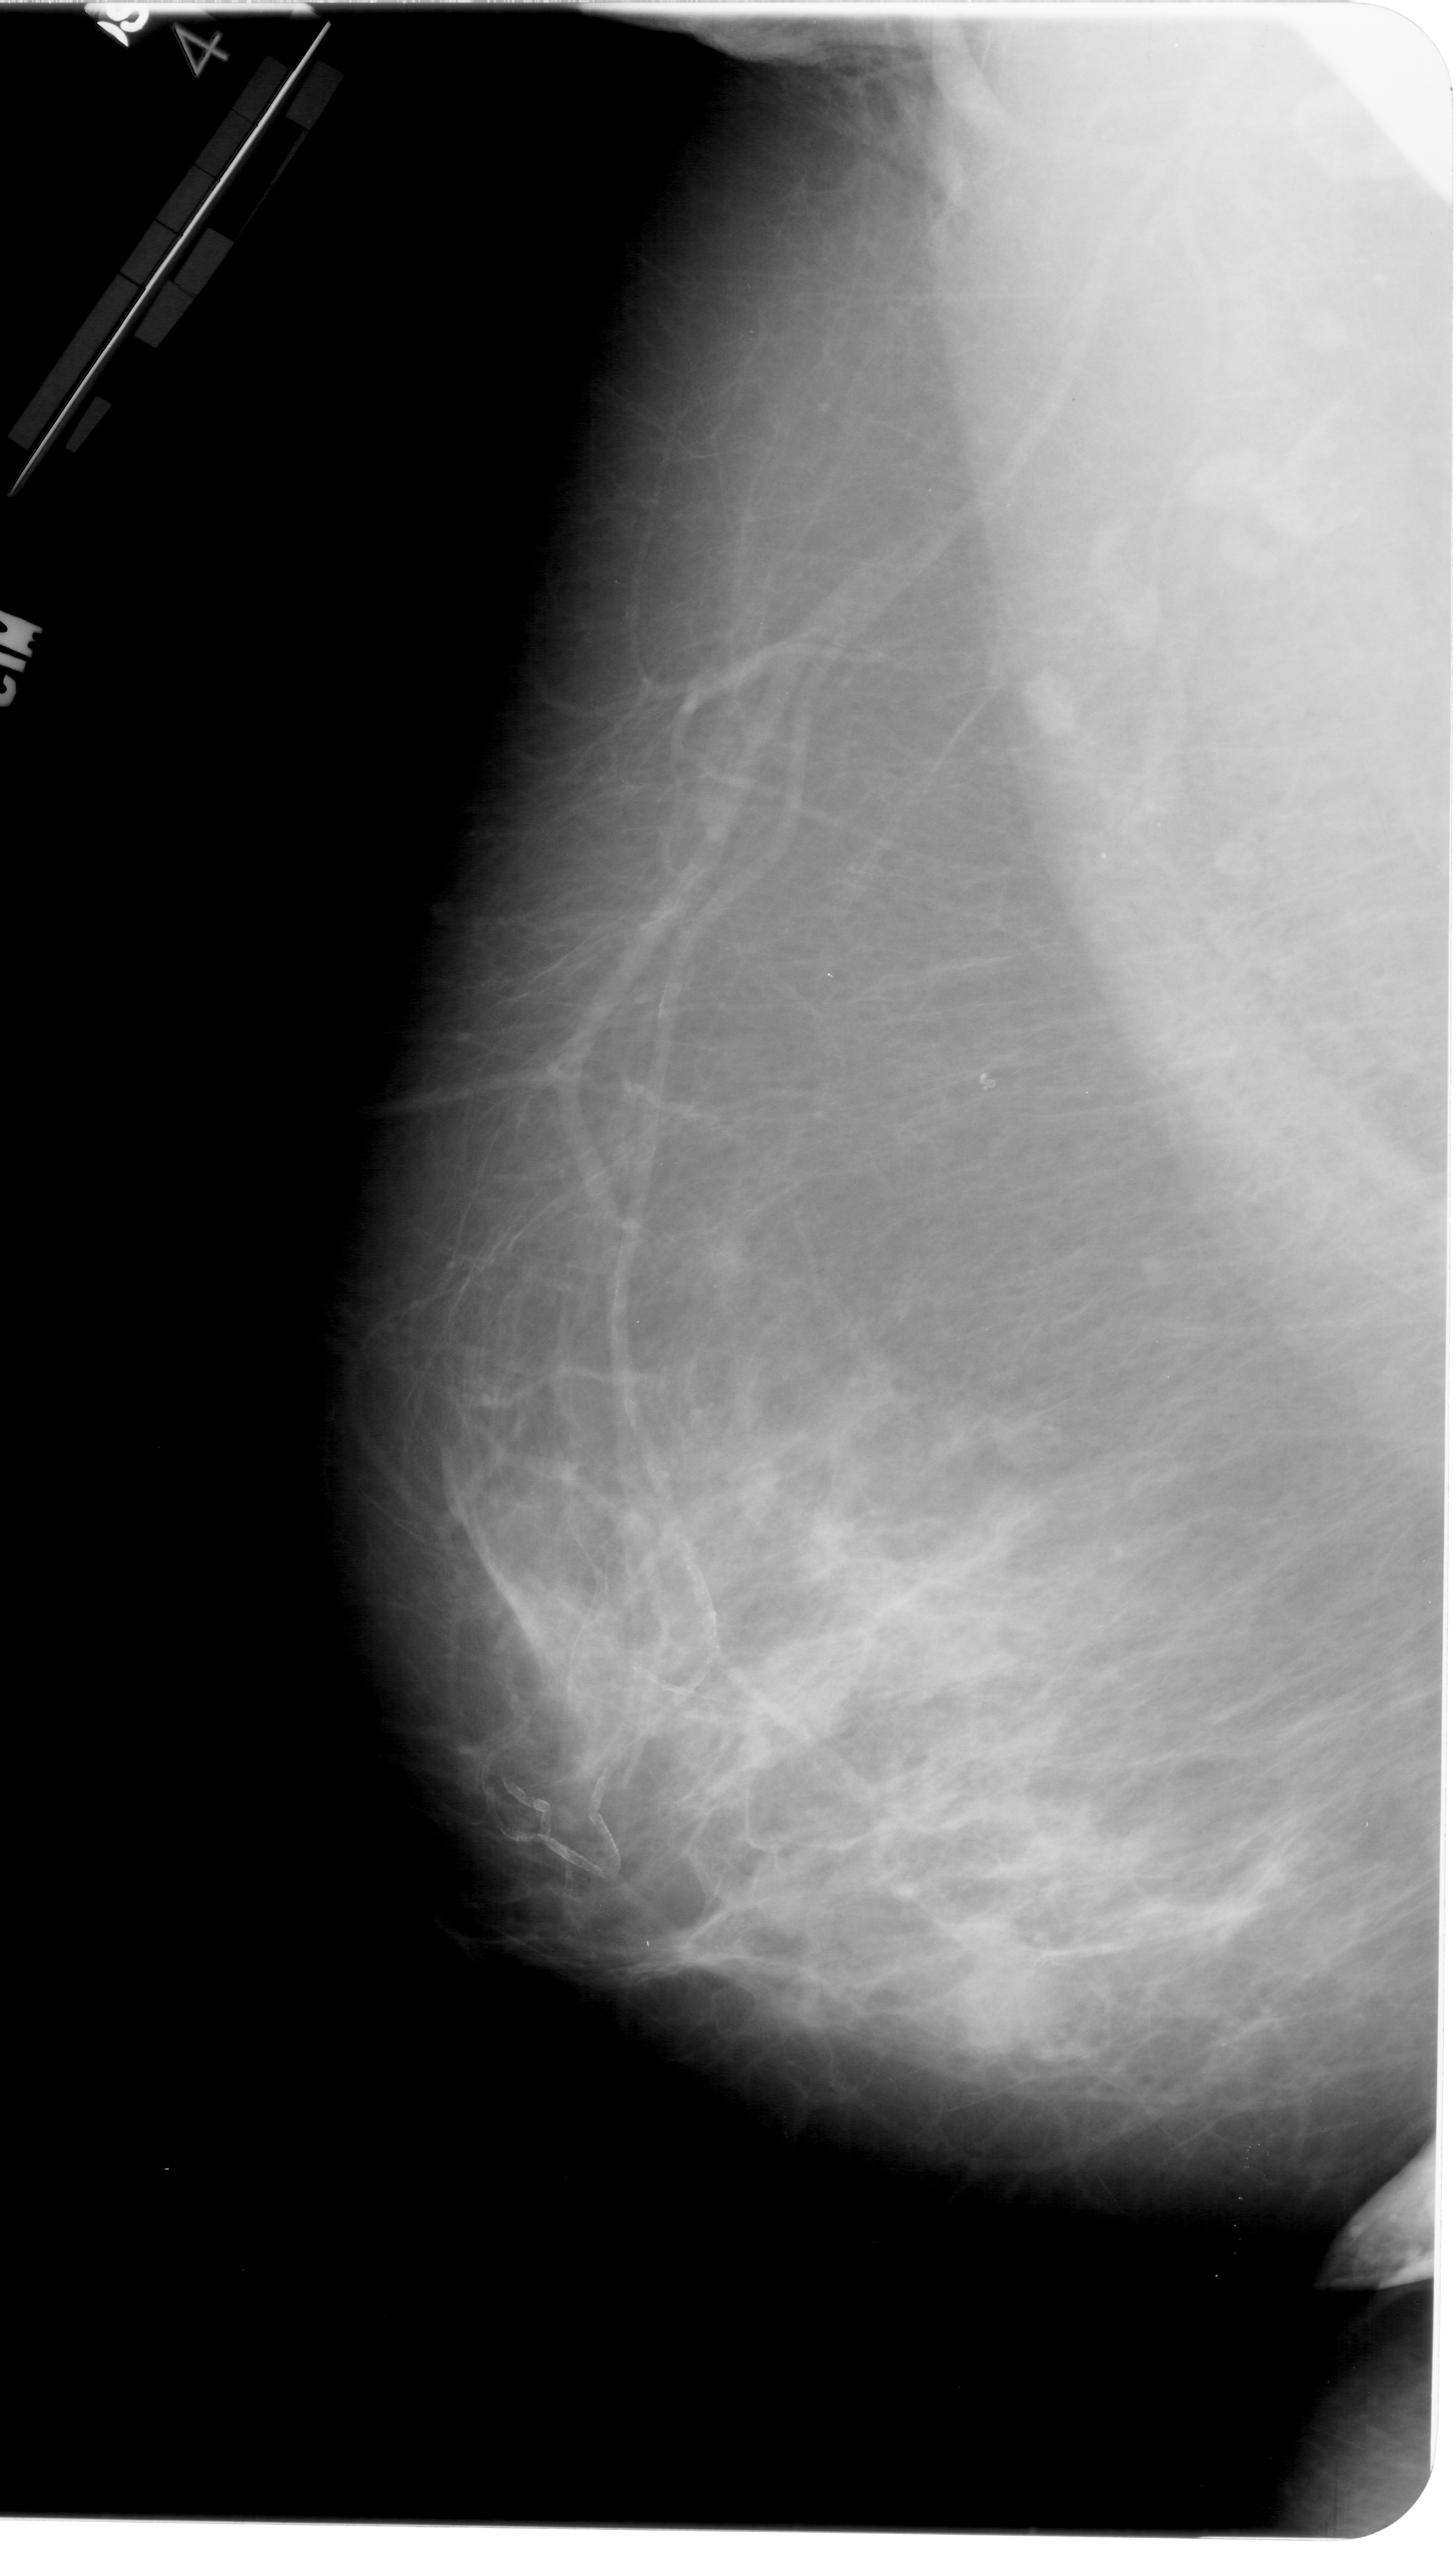
Mammogram (digitized film); left breast; mediolateral oblique (MLO) view; breast composition: heterogeneously dense (BI-RADS density category 3 of 4).
- Abnormality record for this image: mass, shape round, margins ill defined; BI-RADS assessment category 4; pathology result (as recorded, not read from the image): malignant.